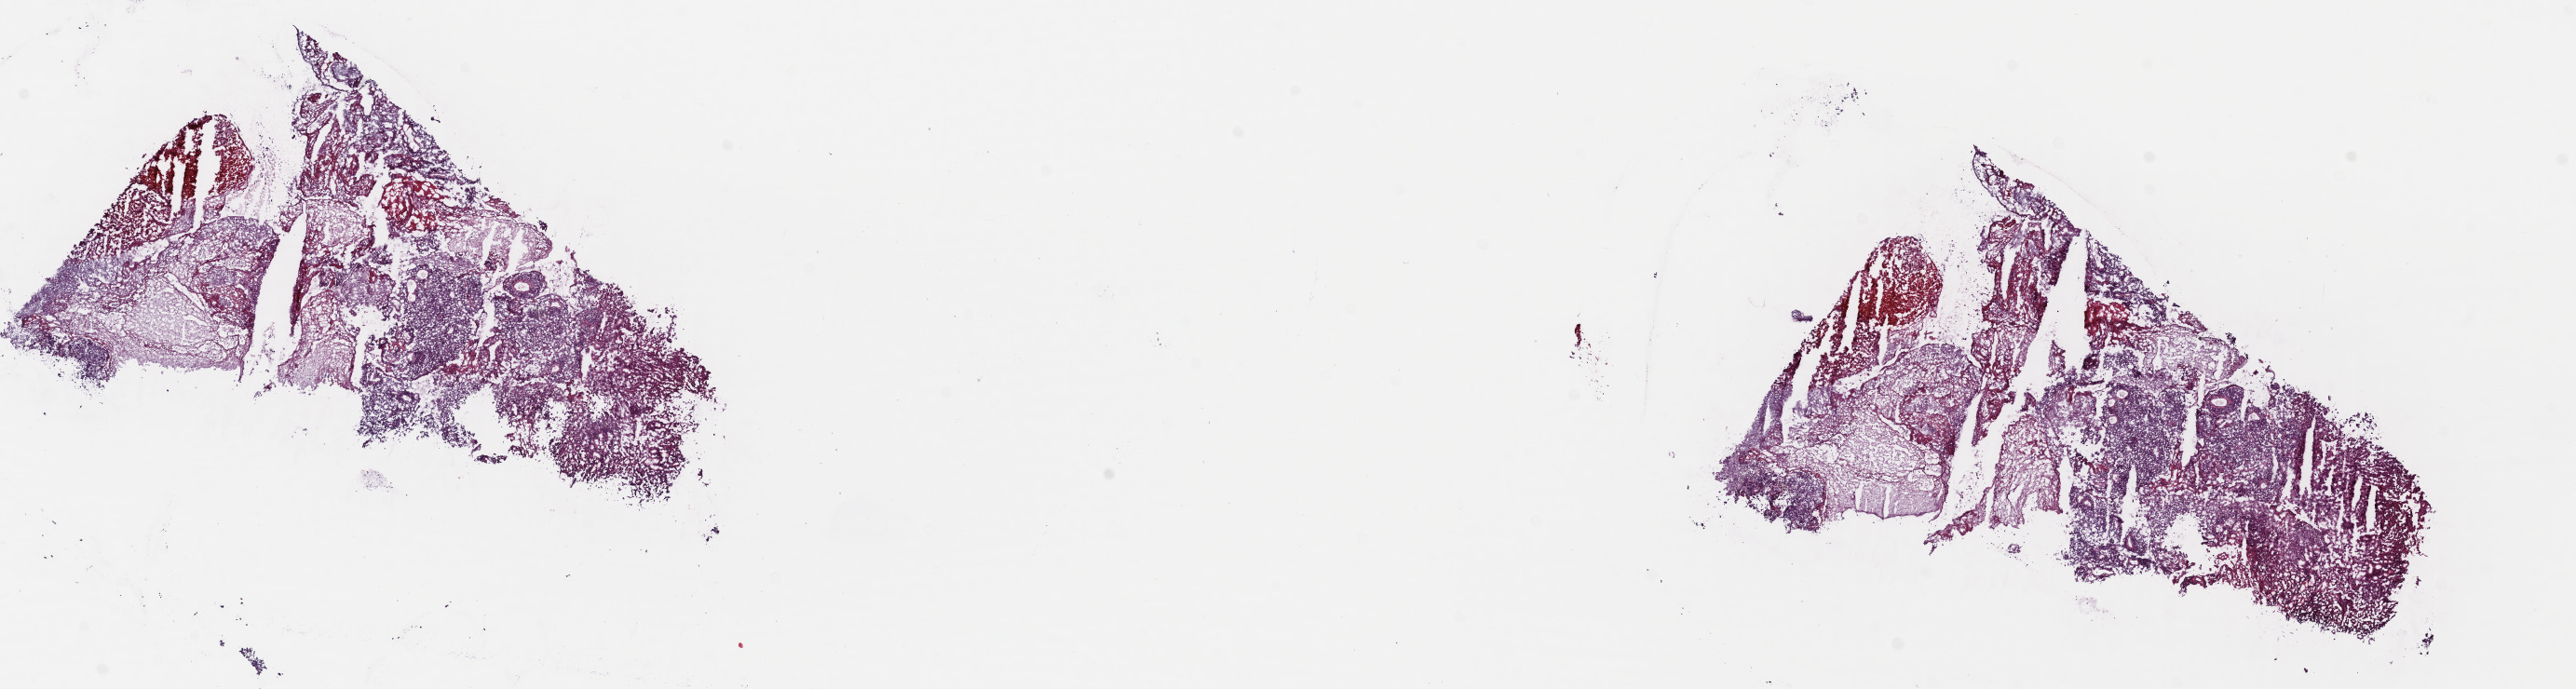
Digitized H&E tissue section (whole slide) — shown as a low-resolution overview of the whole scanned area (about 21.7 x 5.8 mm). Frozen section from the top of the tissue portion. Metastatic tumour sample, sampled site: parietal lobe. Patient: male, age at initial diagnosis 71 years. Composition of this section per pathologist review: tumour cells 80%, tumour nuclei 90%, normal cells 0%, stromal cells 20%, necrosis 0%. Inflammatory infiltration, as recorded: lymphocyte infiltration 0%, monocyte infiltration 0%, neutrophil infiltration 0%.
This section: metastatic tumour tissue. Patient diagnosis: Malignant melanoma, NOS.